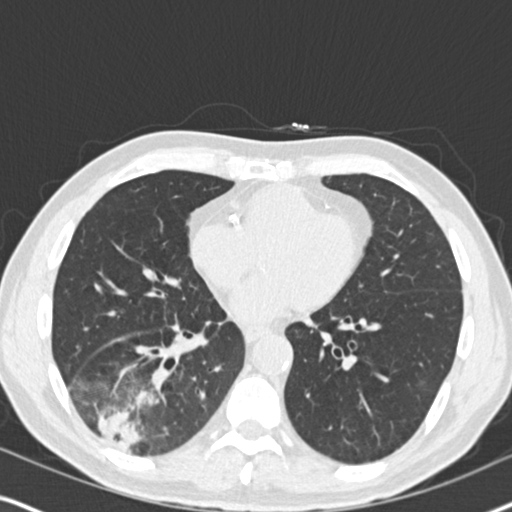
Low-dose screening chest CT, axial slice. Second screening round (one year after baseline). Lung window (W 1500 / L -600 HU). 2 mm slice thickness. Slice 101 of 182 in the series. Male participant, aged 61 years at enrolment. Current smoker at enrolment.
- Expert-annotated lung lesion, box from (x=59, y=340) to (x=192, y=467) px.
- Screening reader's record for this exam (one nodule recorded; not confirmed to be the boxed lesion): non-calcified nodule or mass ≥4 mm, right lower lobe, 90 × 80 mm, soft tissue attenuation, pre-existing on the prior screen: yes; interval growth: yes.
- Official screen result: positive, other.
- Participant outcome: lung cancer diagnosed 20 days after this screen — bronchiolo-alveolar adenocarcinoma, NOS, right lower lobe, moderately differentiated (G2), stage IIIB (AJCC 6th edition), 90 mm at pathology.